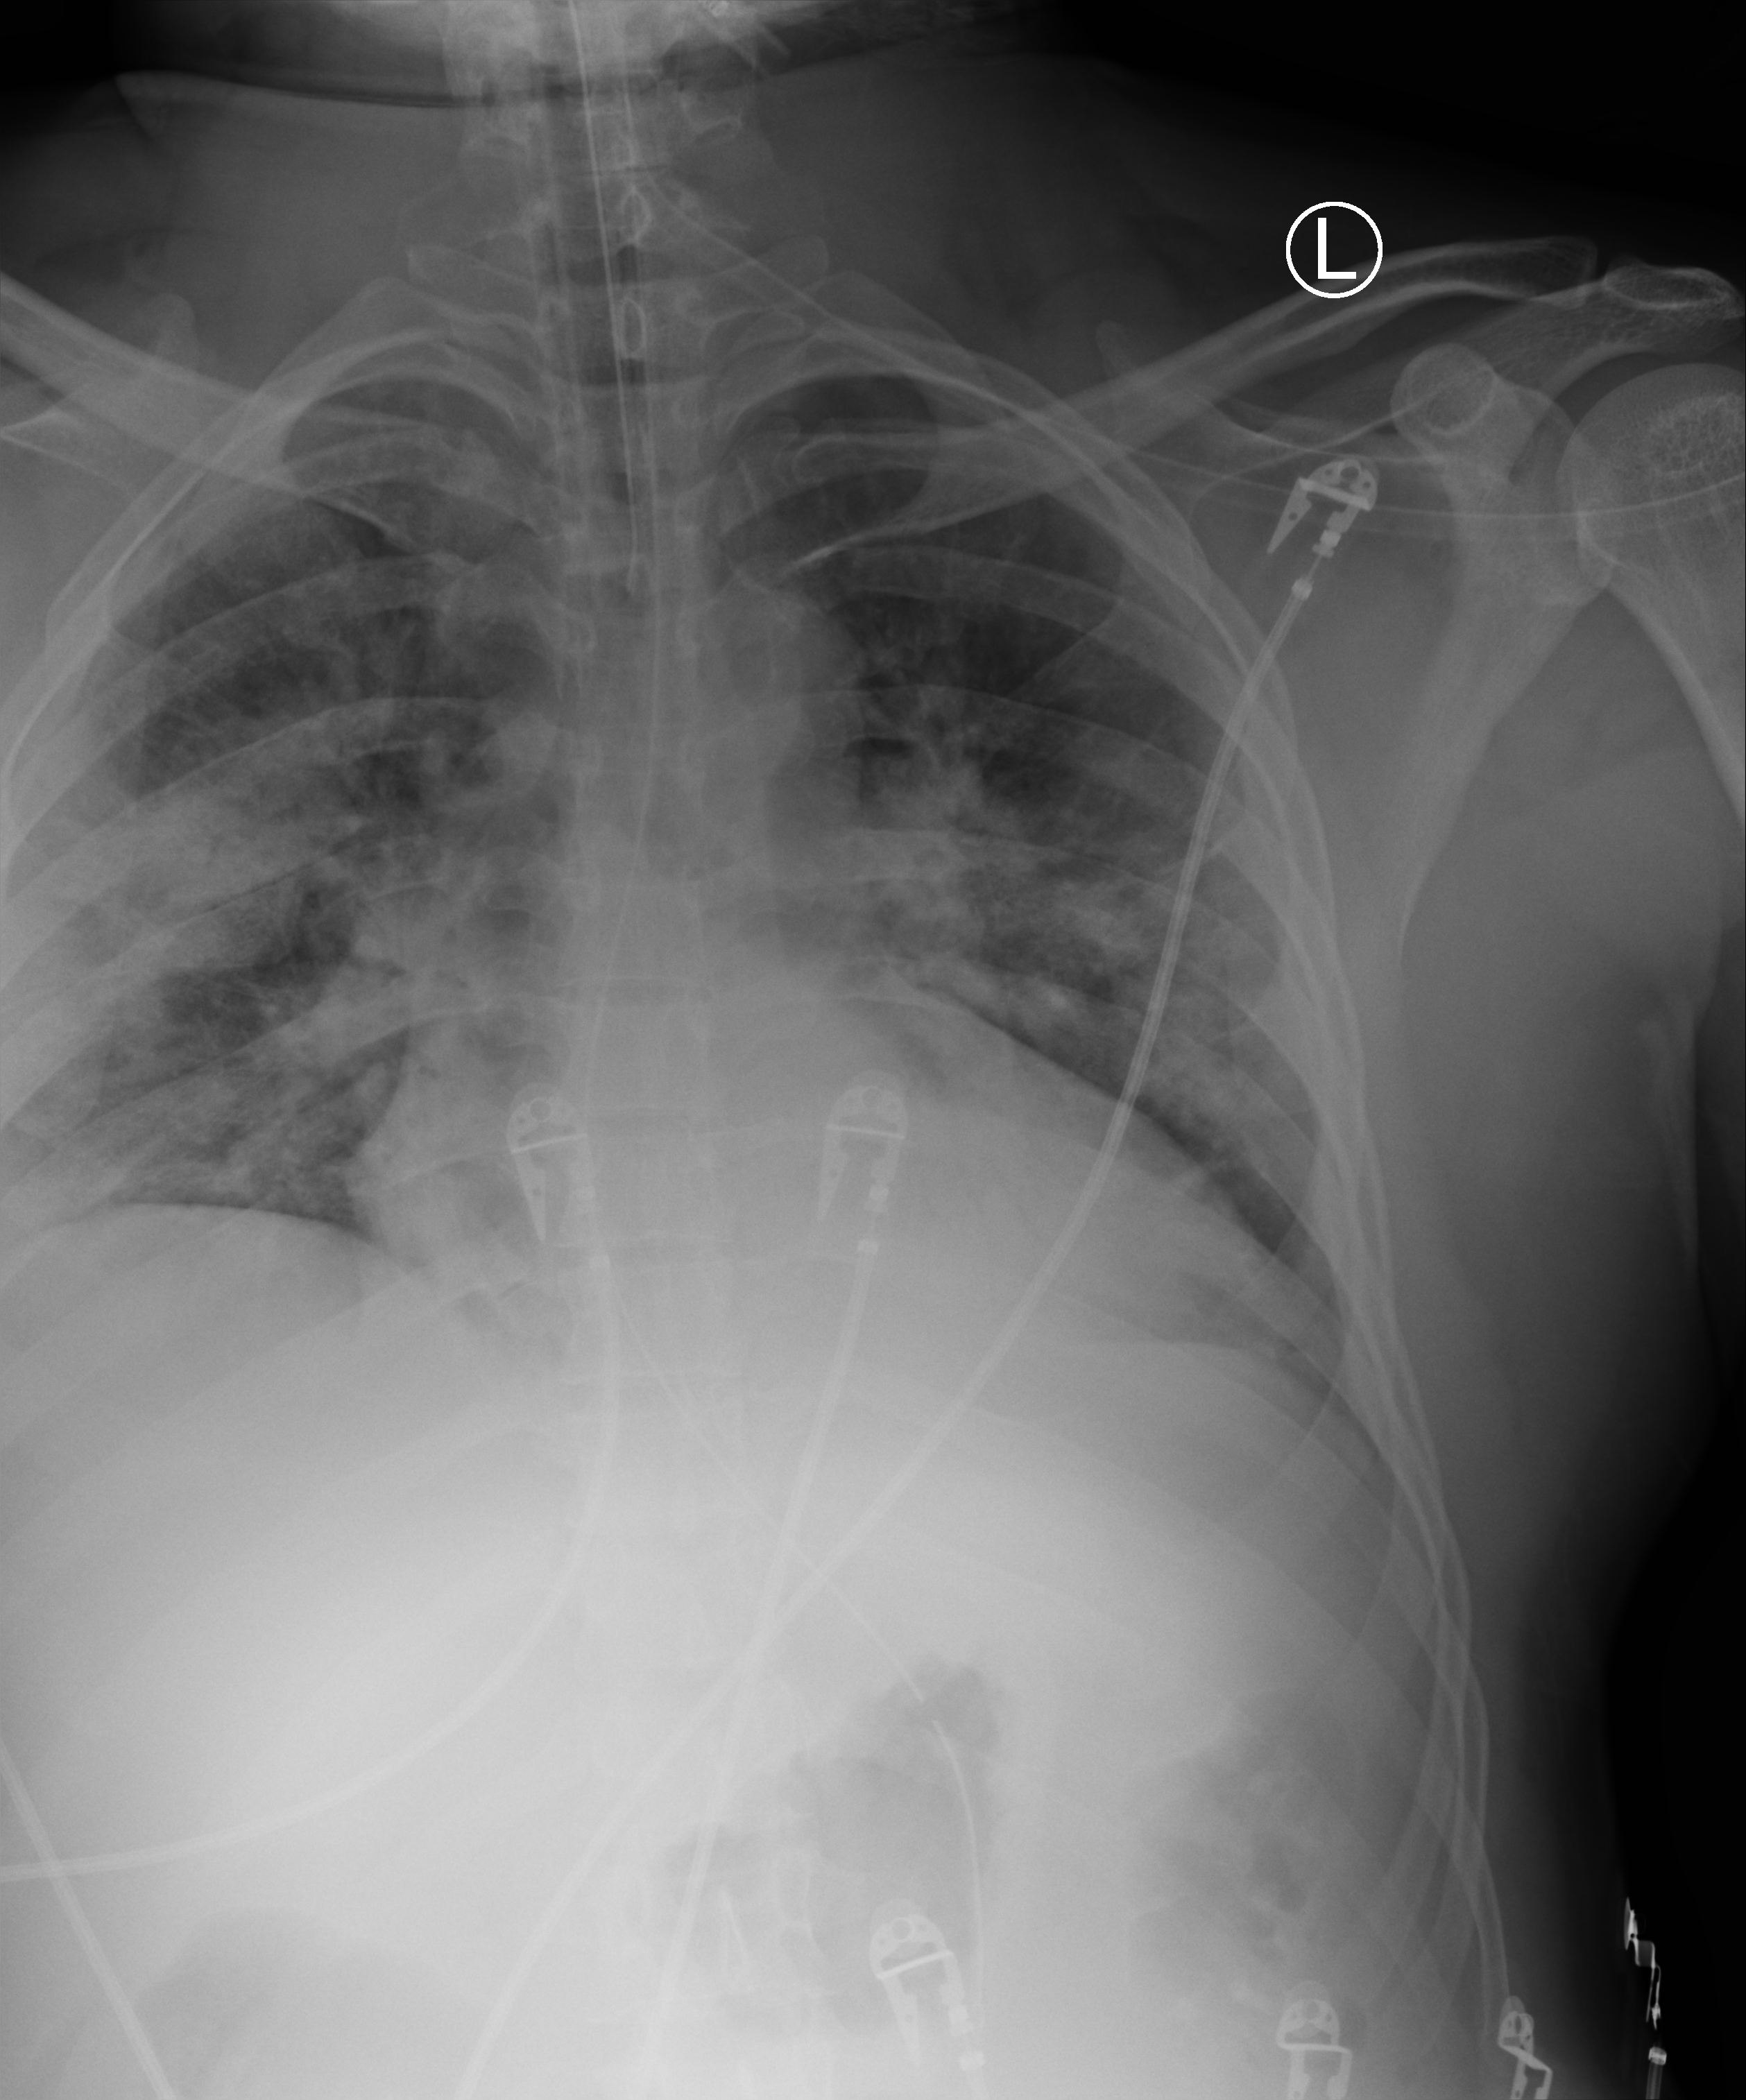
Chest X-ray (portable); anteroposterior (AP) projection. Male patient hospitalised with COVID-19, age 18–59 years.
From the hospital-stay record, not from the radiograph (when in the stay this image was taken is not recorded): COPD (admission record): no.